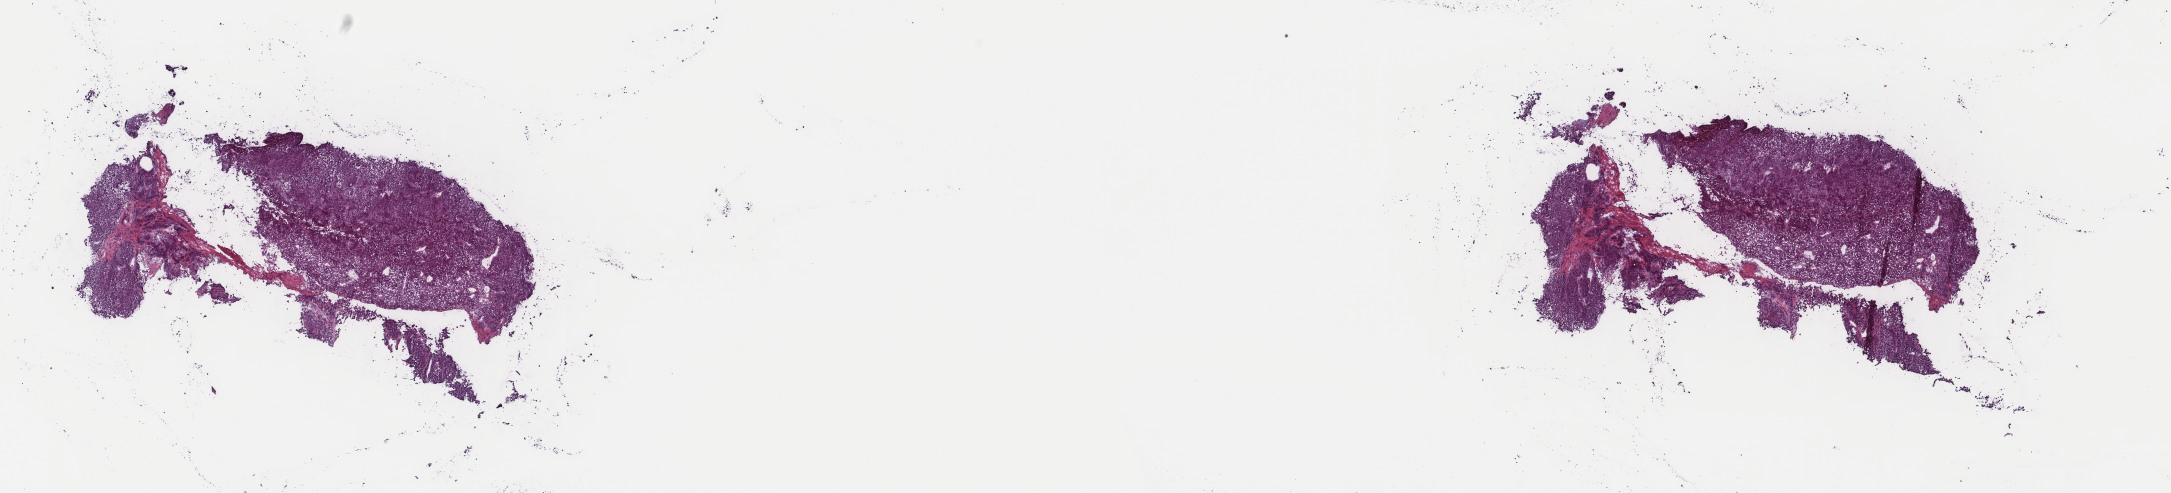
Whole-slide histology image, H&E — whole scanned area (about 17.2 x 3.9 mm, slide scanned at 40x) shown as a low-resolution overview. Frozen section from the top of the tissue portion. Adrenal cortex, primary tumour sample. Patient: male, age at initial diagnosis 47 years. Composition of this section per pathologist review: tumour cells 90%, tumour nuclei 100%, normal cells 0%, stromal cells 10%, necrosis 0%. Inflammatory infiltration, as recorded: lymphocyte infiltration 1%, monocyte infiltration 0%, neutrophil infiltration 0%.
Pathologic diagnosis: Adrenal cortical carcinoma (cortex of adrenal gland).